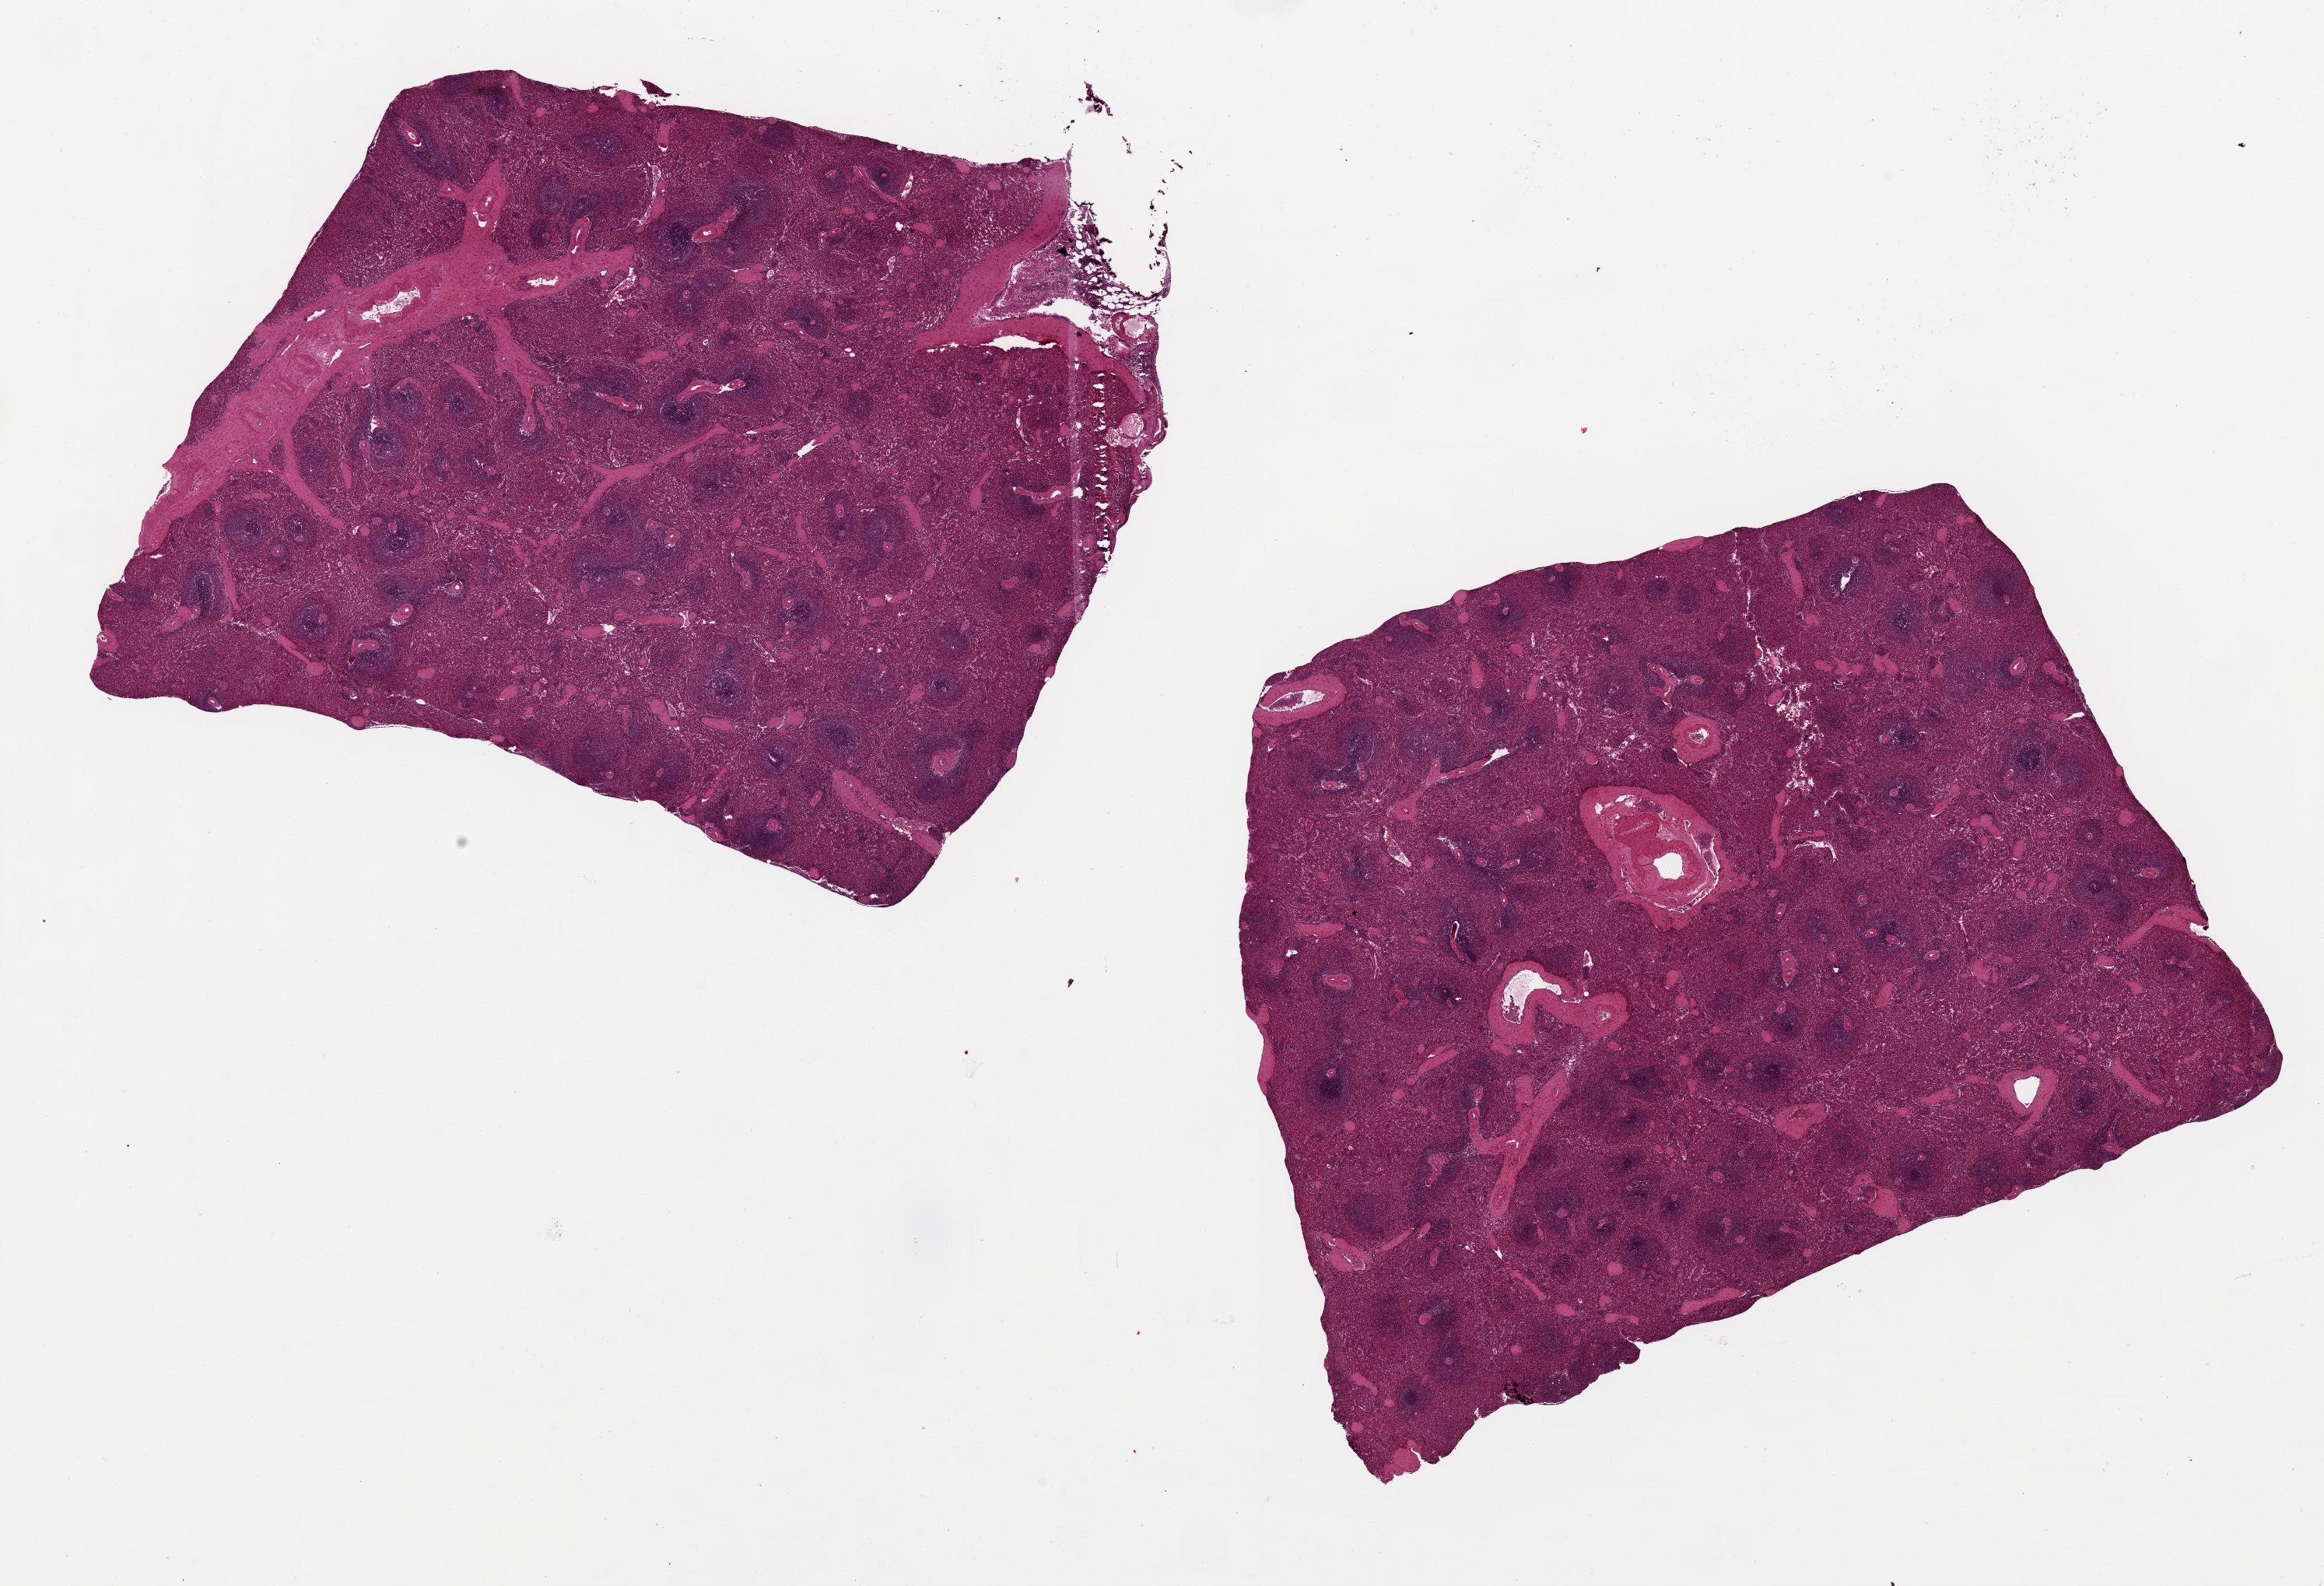
Digitized haematoxylin and eosin-stained section — whole scanned area (about 23.6 x 16.1 mm, acquisition: 20x scan) shown as a low-resolution overview; PAXgene-fixed, paraffin-embedded tissue; section of spleen (target tissue); donor tissue sample. Donor: female.
Pathologist's review note for this sample: 2 aliquots, ~8x7mm.